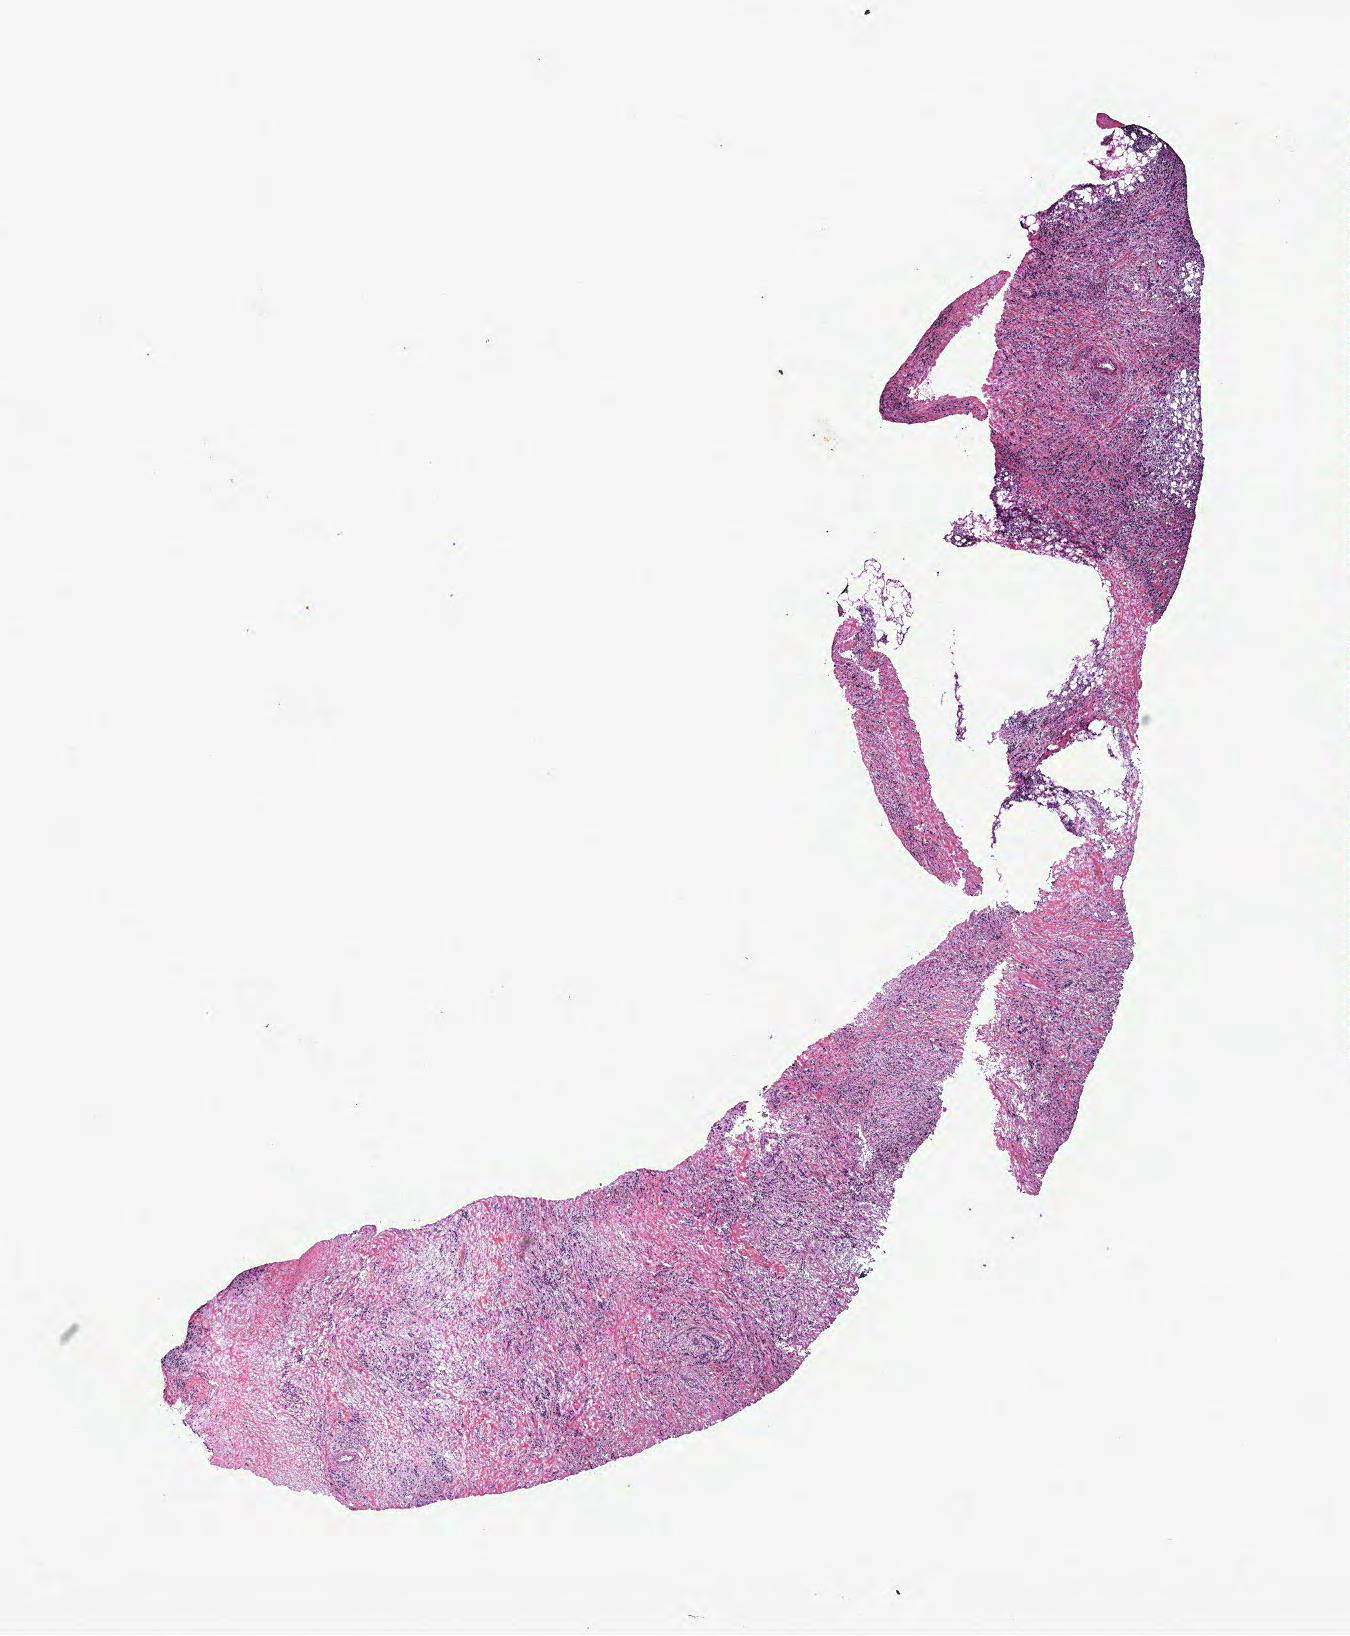
Digitized H&E tissue section (whole slide) — a low-resolution overview of the entire scanned area, about 10.8 x 13.1 mm (acquisition: 40x scan); breast, tumour tissue. 40-year-old female patient.
- AJCC pathologic stage: III
- diagnosis: Infiltrating lobular carcinoma, NOS